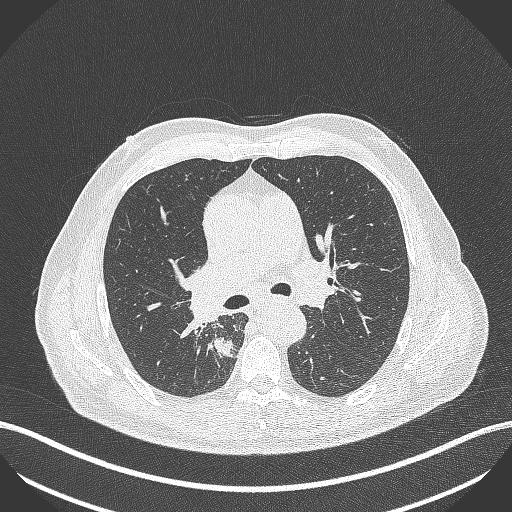
Chest CT, one axial slice. Position 284 of 451 along the scan axis. Reconstruction kernel B70f. 100 kVp. Lung window (W 1500 / L -600 HU). 1 mm slice thickness. 512 × 512 image matrix, field of view 400 × 400 mm. Male patient, age 61 years. From the clinical record (not read from this slice): clinical TNM (as recorded): T1 N0 M0; histopathological grade: G3.
Structures marked on this image (rectangle marked by the reading radiologist):
- lung tumour (recorded histology: small cell carcinoma): box from (x=212, y=335) to (x=239, y=362) px